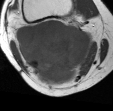
MRI of an extremity soft-tissue mass, one axial slice; position 27 of 45 along the scan axis; MR volume resampled by the dataset authors to the PET/CT grid (not the native acquisition matrix); 3.27 mm slice thickness; 113 × 111 image matrix, field of view 110 × 108 mm. Female patient. From the clinical record (not read from this slice): histological type: liposarcoma; site of the primary tumour: right thigh.
Annotated regions visible in this slice (expert contour drawn on MRI and transferred to this co-registered scan by the dataset authors):
- gross tumour volume (mass): bounding box <17,19,95,86> (left, top, right, bottom; pixels)